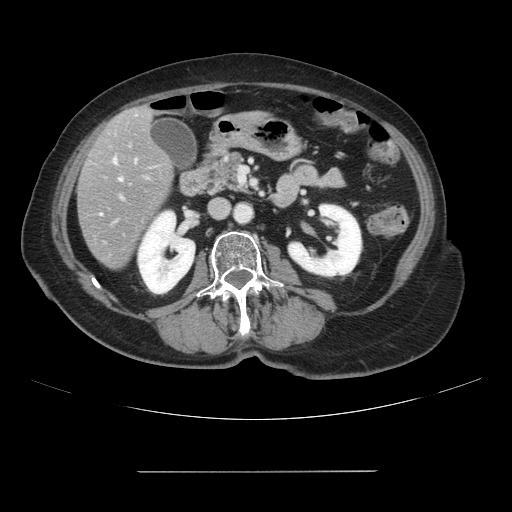
Contrast-enhanced abdominal CT, one axial slice. Slice 28 of 111 in the series (ordered by position). Intravenous contrast given. Soft-tissue window (W 400 / L 40 HU). 2.5 mm slice thickness. 512 × 512 image matrix, field of view 400 × 400 mm. Female patient, age 74 years. Case-level facts recorded for this patient, not image findings: diagnosis: colorectal cancer liver metastases, imaged before liver resection; multiple liver metastases: yes; largest metastasis: 1.1 cm; disease in both lobes: yes.
Structures marked on this image (manually delineated by an expert):
- hepatic veins: bounding box [x1, y1, x2, y2] px = [114, 160, 121, 180]
- liver: [78, 107, 173, 269]
- planned liver remnant (the part of the liver to remain after resection): [142, 108, 153, 119]